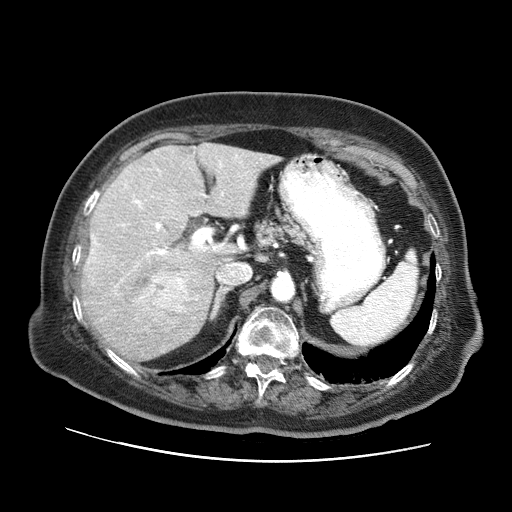
Contrast-enhanced abdominal CT (liver protocol), one axial slice. Slice 42 of 73 in the series (ordered by position). 120 kVp. Soft-tissue window (W 400 / L 40 HU). 2.5 mm slice thickness. 512 × 512 image matrix. Case-level facts recorded for this patient, not image findings: diagnosis: hepatocellular carcinoma (patient treated with transarterial chemoembolisation; whether this scan precedes or follows treatment is not stated here); TNM stage (as recorded): Stage-I; Child-Pugh class: A; tumour differentiation: well differentiated; tumour nodularity: uninodular.
Structures marked on this image (semi-automatically segmented with operator editing):
- liver parenchyma outside the tumour (the mass and vessels are separate outlines, so this box may not span the whole liver): bounding box <82,142,279,360> (left, top, right, bottom; pixels)
- mass: <133,266,195,332>
- liver vessels: <91,155,238,281>